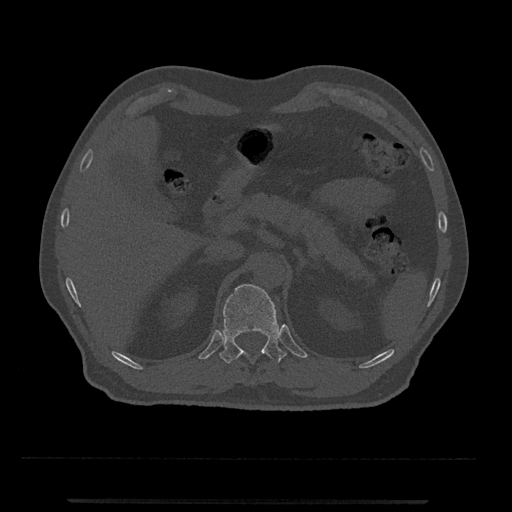
CT including the spine, one axial slice; position 412 of 797 along the scan axis; reconstruction kernel Br40s/3; 120 kVp; bone window (W 1800 / L 400 HU); 0.5 mm slice thickness; 512 × 512 image matrix, field of view 419 × 419 mm. Male patient, age 63 years. Case-level facts recorded for this patient, not image findings: primary cancer: prostate.
Annotated regions visible in this slice (semi-automatically segmented with operator editing):
- T12 vertebra: bounding box (x1, y1, x2, y2) in pixels: (219, 284, 287, 364)